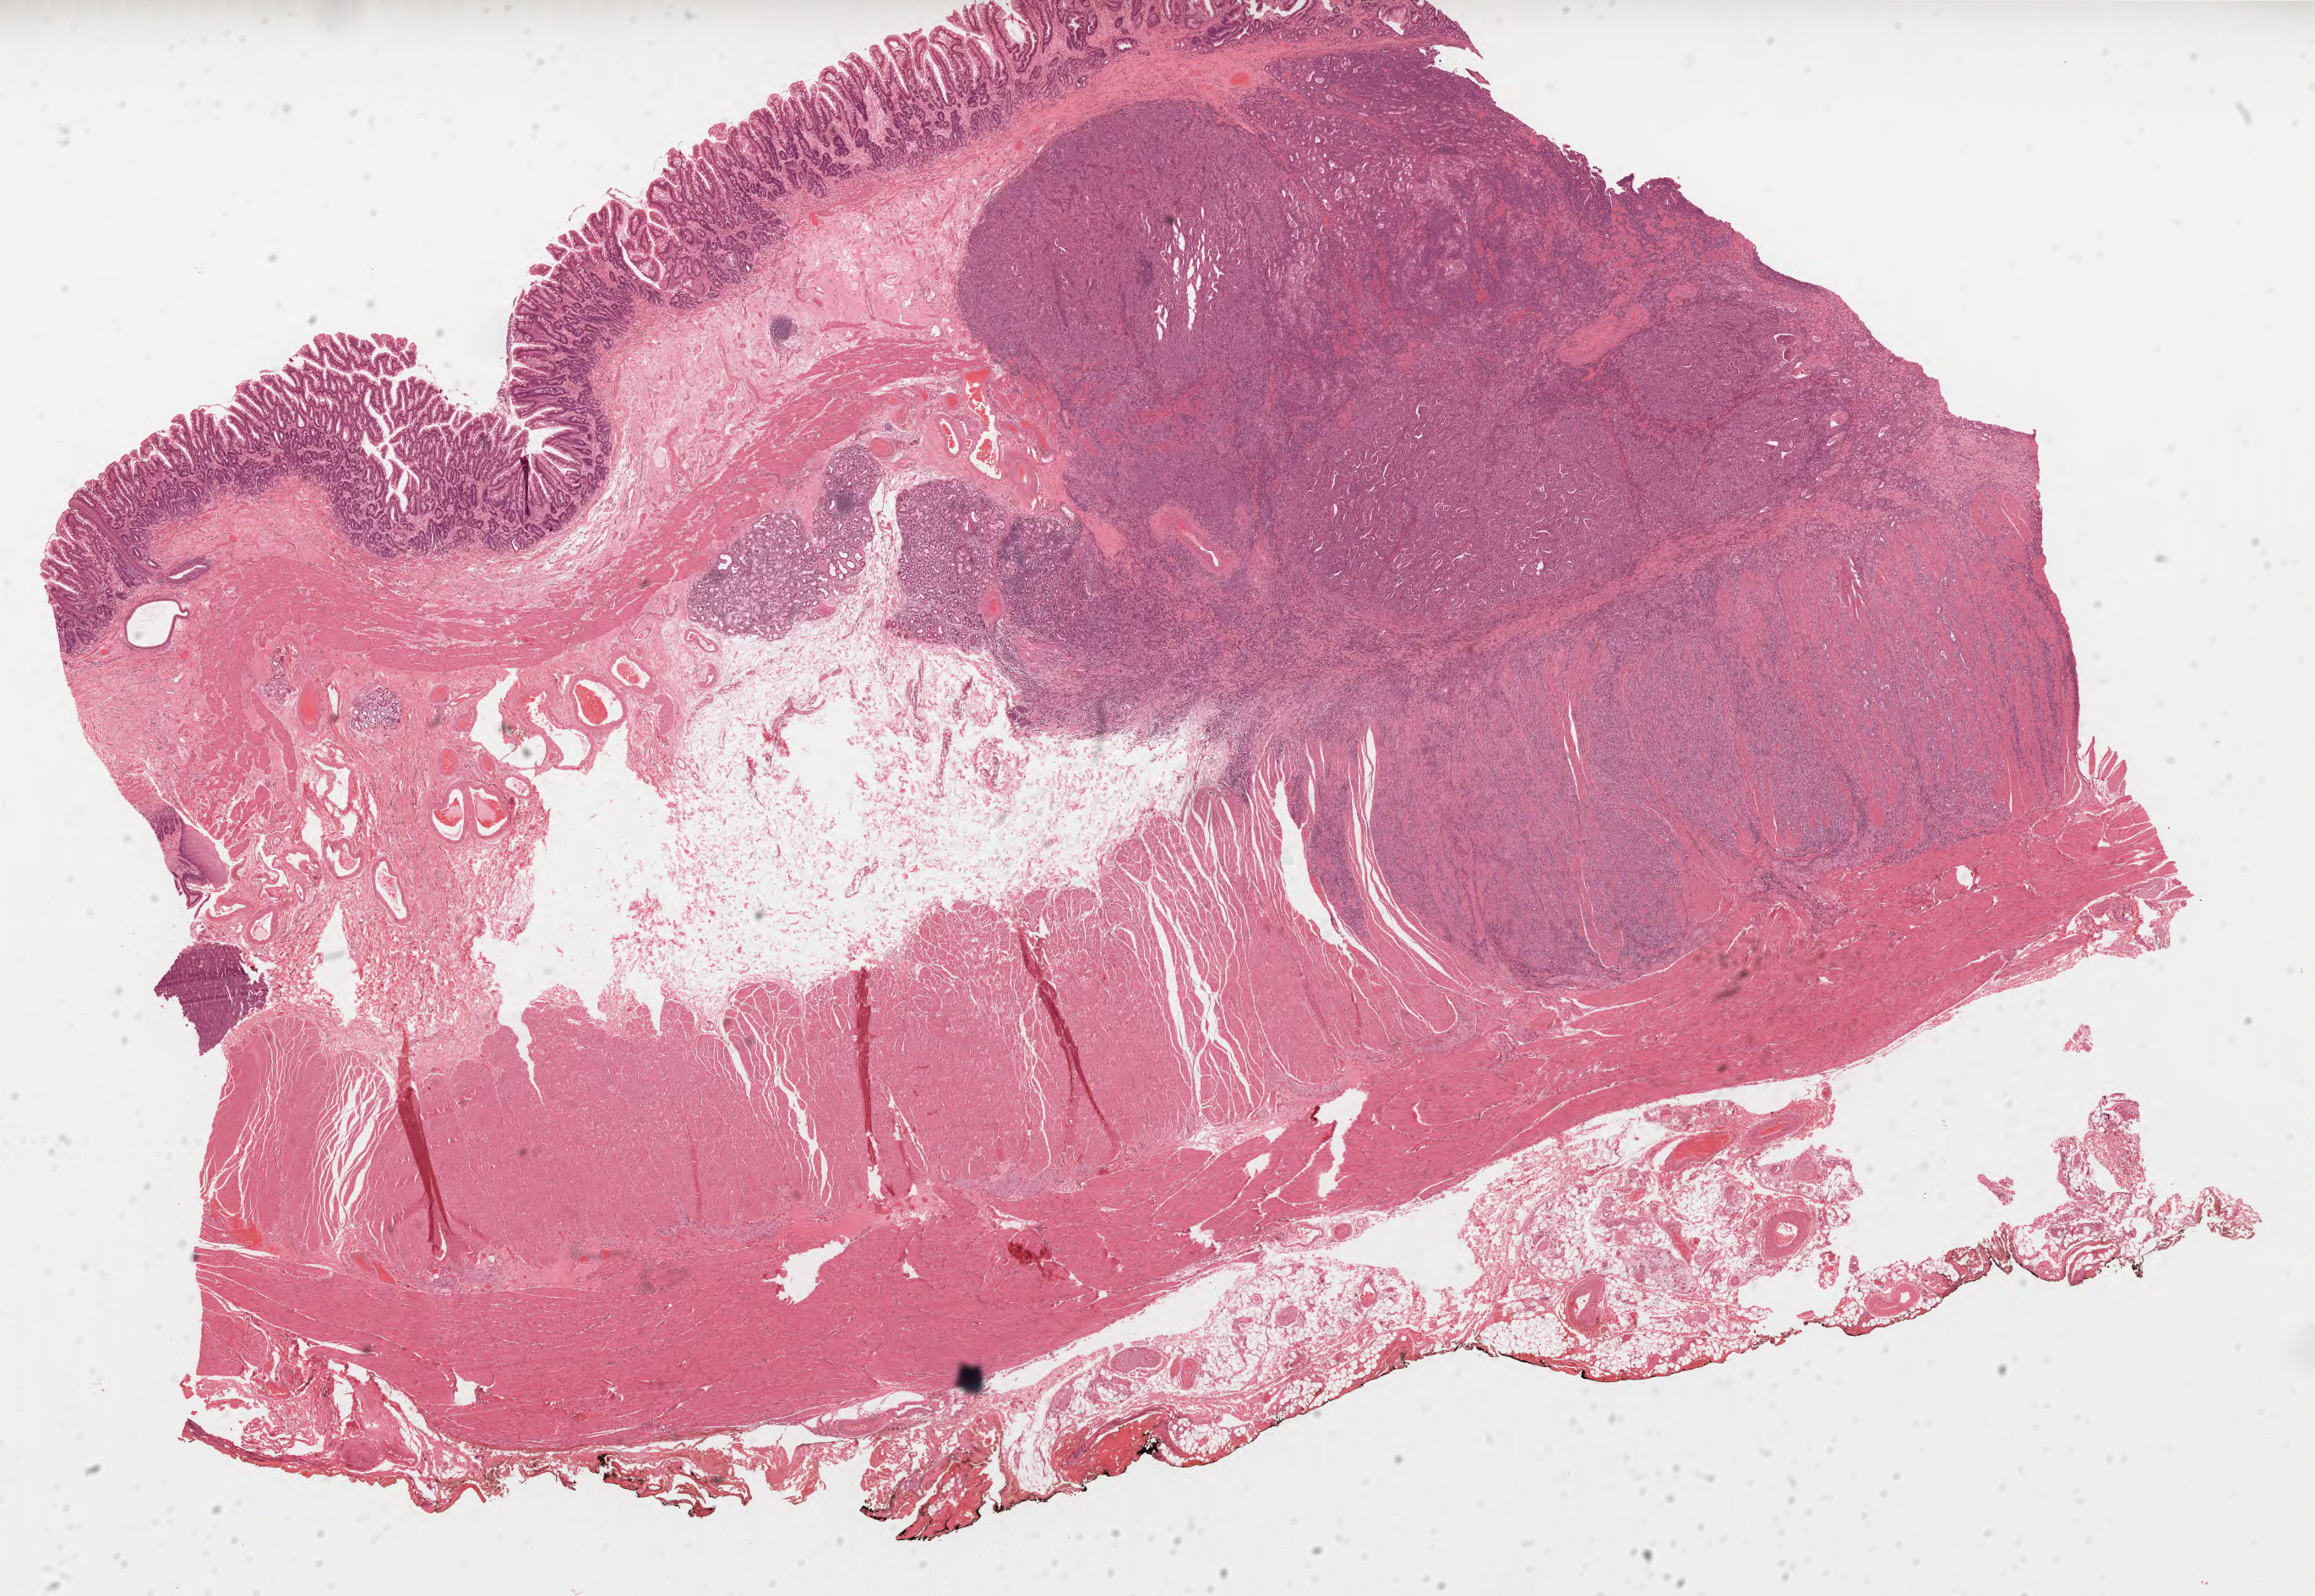
Digitized H&E tissue section (whole slide), low-resolution overview of the scanned area, about 22.1 x 15.2 mm (from a 40x scan); FFPE section; primary tumour sample from the esophagus. Male, age 75 years at initial diagnosis.
Pathologic diagnosis: Adenocarcinoma, NOS (cardia, NOS).